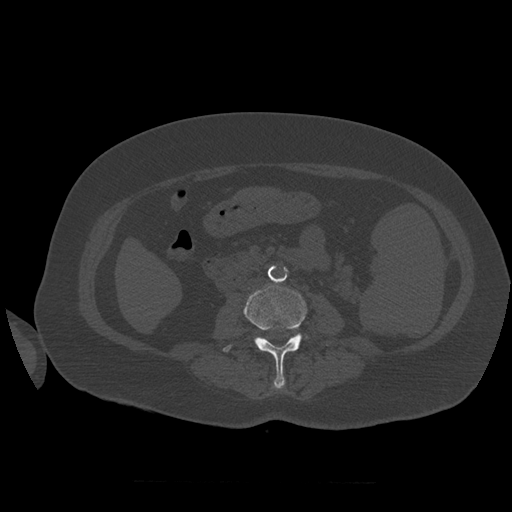
CT including the spine, one axial slice; slice 227 of 399 in the series (ordered by position); reconstruction kernel STANDARD; bone window (W 1800 / L 400 HU); 1.25 mm slice thickness; 512 × 512 image matrix, field of view 404 × 404 mm. Patient age 81 years. From the clinical record (not read from this slice): primary cancer: renal; vertebrae with lytic lesions (as recorded): L1.
Outlined on this slice (semi-automatic segmentation, software-assisted and operator-edited):
- L3 vertebra: box from (x=223, y=286) to (x=307, y=389) px